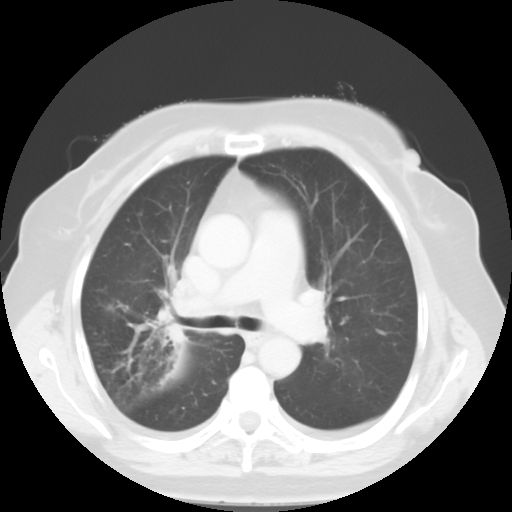
Chest CT, one axial slice. Slice 33 of 52 in the series (ordered by position). Reconstruction kernel STANDARD. Lung window (W 1500 / L -600 HU). 5 mm slice thickness. 512 × 512 image matrix. Patient: female, 81 years. From the clinical record (not read from this slice): clinical TNM (as recorded): T4 N3 M1b.
Outlined on this slice (bounding box drawn by a radiologist):
- lung tumour (recorded histology: adenocarcinoma): box from (x=157, y=303) to (x=188, y=348) px